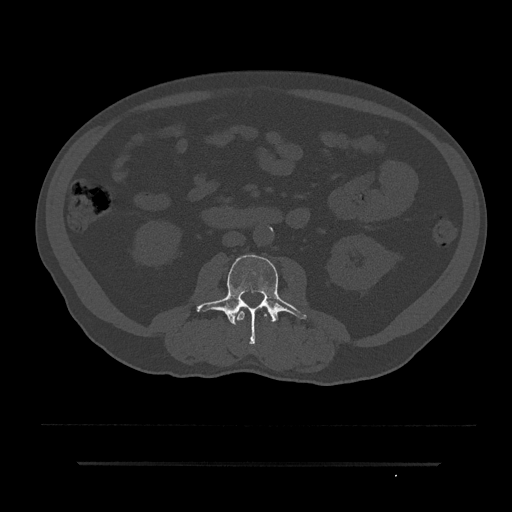
CT including the spine, one axial slice; slice 15 of 797 in the series (ordered by position); bone window (W 1800 / L 400 HU); 0.5 mm slice thickness; 512 × 512 image matrix, field of view 464 × 464 mm. Male patient, age 59 years. From the clinical record (not read from this slice): primary cancer: bile ducts; vertebrae with lytic lesions (as recorded): T10.
Annotated regions visible in this slice (semi-automatically segmented with operator editing):
- L2 vertebra: bounding box [x1, y1, x2, y2] px = [234, 308, 268, 321]
- L3 vertebra: [196, 255, 307, 344]